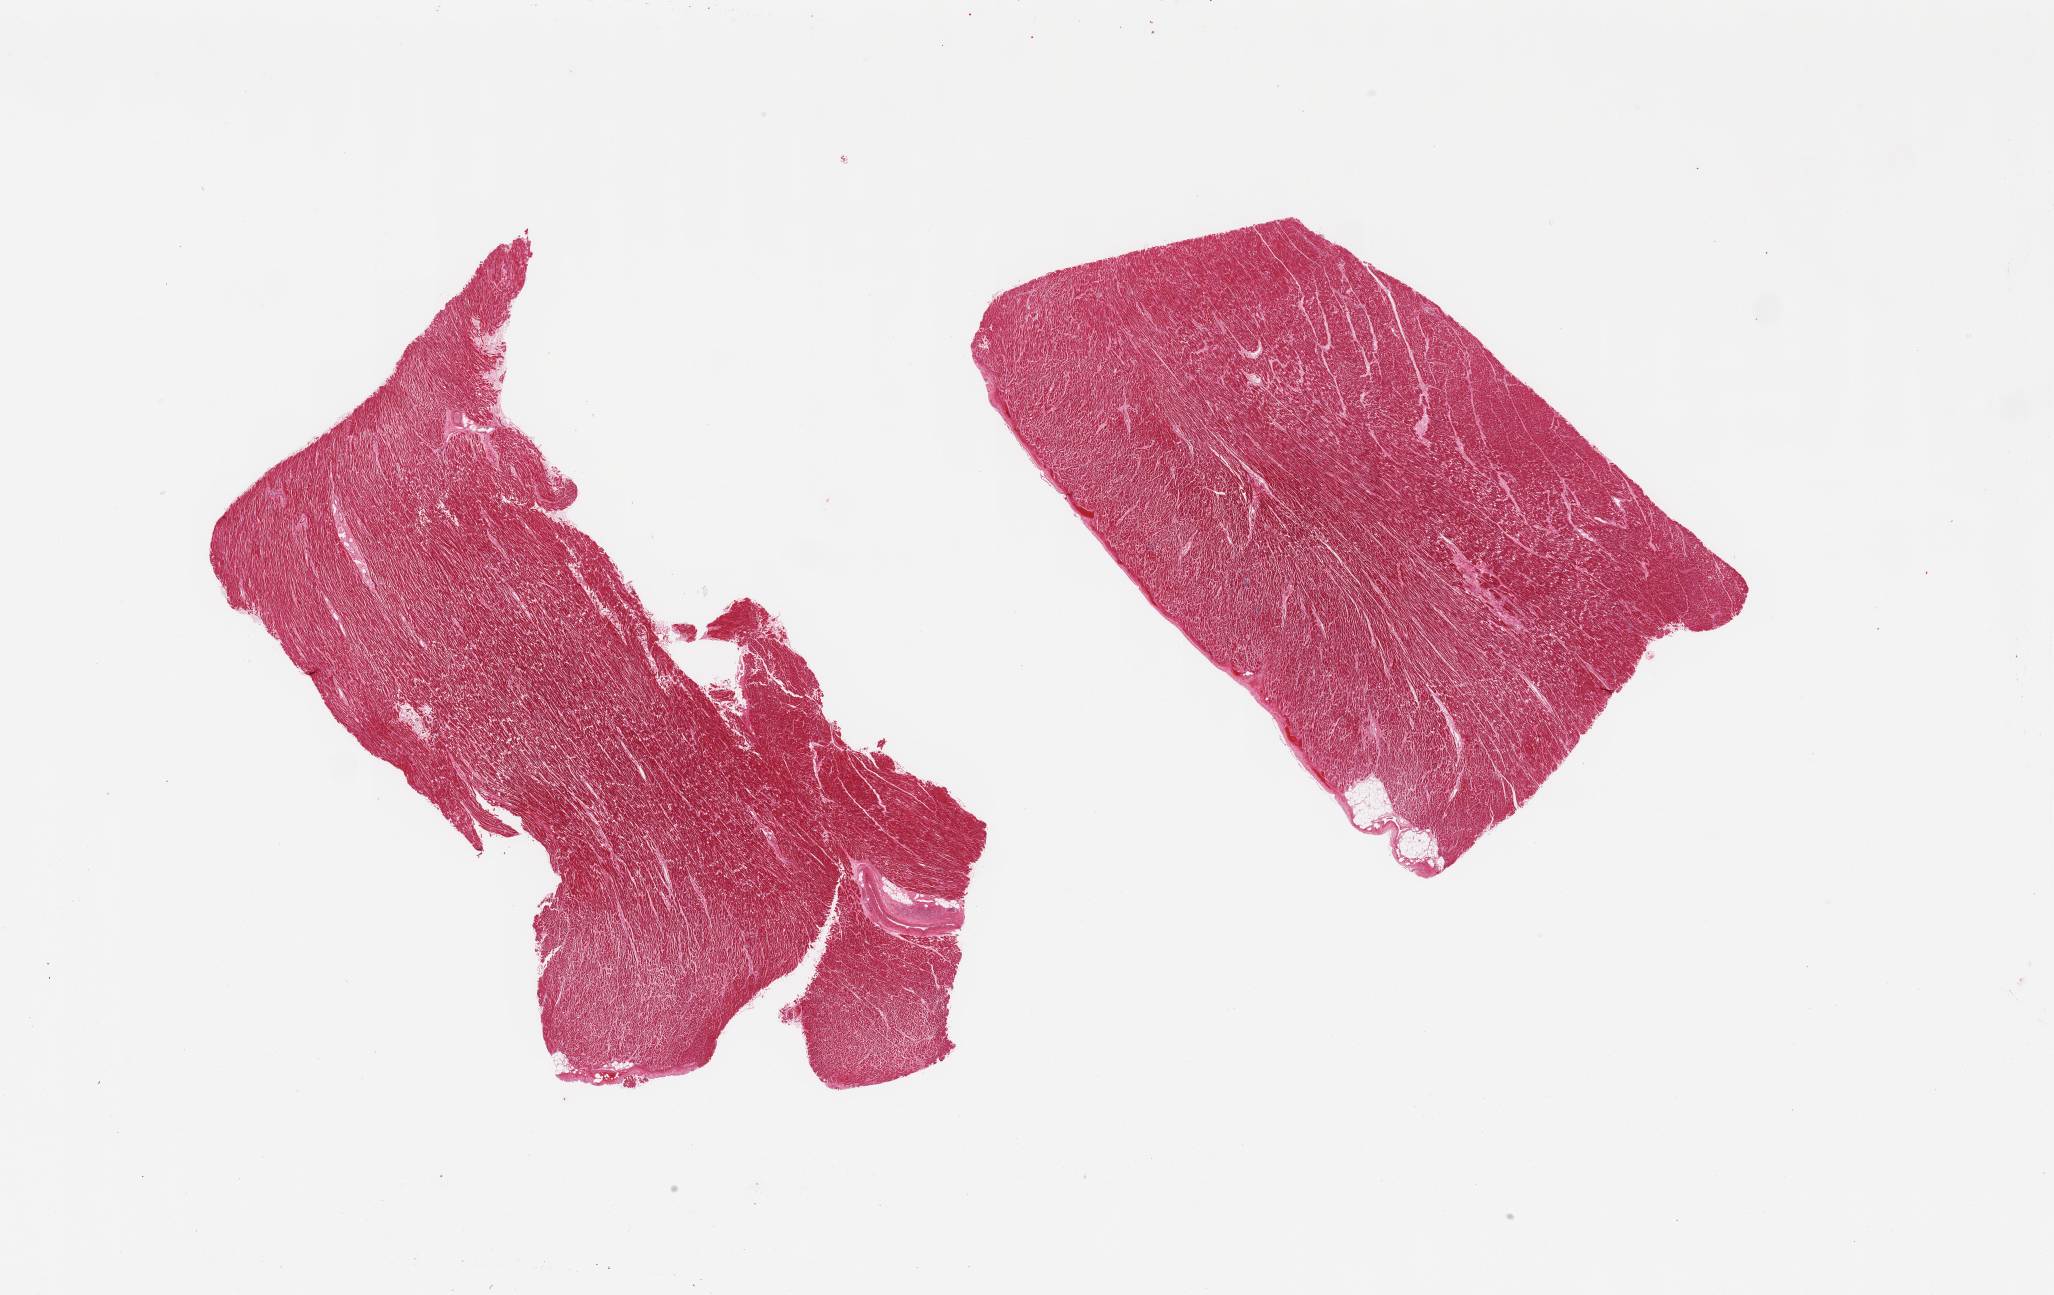
Digitized hematoxylin and eosin (H&E)-stained section, brightfield, low-resolution overview of the scanned area, about 32.5 x 20.5 mm (acquisition: 20x scan); PAXgene-fixed paraffin-embedded (PFPE) section; target tissue: heart; tissue donor sample. Donor: male.
* review note (as recorded): 2 pieces; fragmented enlarged myofibers